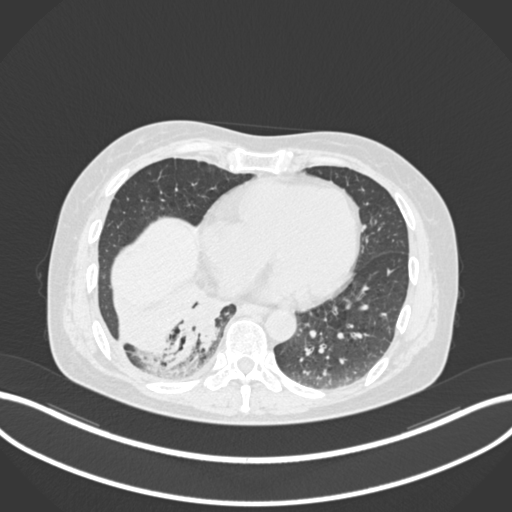
Chest CT, one axial slice. Slice 47 of 168 in the series (ordered by position). 120 kVp. Lung window (W 1500 / L -600 HU). 512 × 512 image matrix, field of view 400 × 400 mm. Female patient, age 63 years. From the clinical record (not read from this slice): clinical TNM (as recorded): T1c N0 M0.
Outlined on this slice (rectangle marked by the reading radiologist):
- lung tumour (recorded histology: adenocarcinoma): bounding box (x1, y1, x2, y2) in pixels: (170, 289, 227, 365)